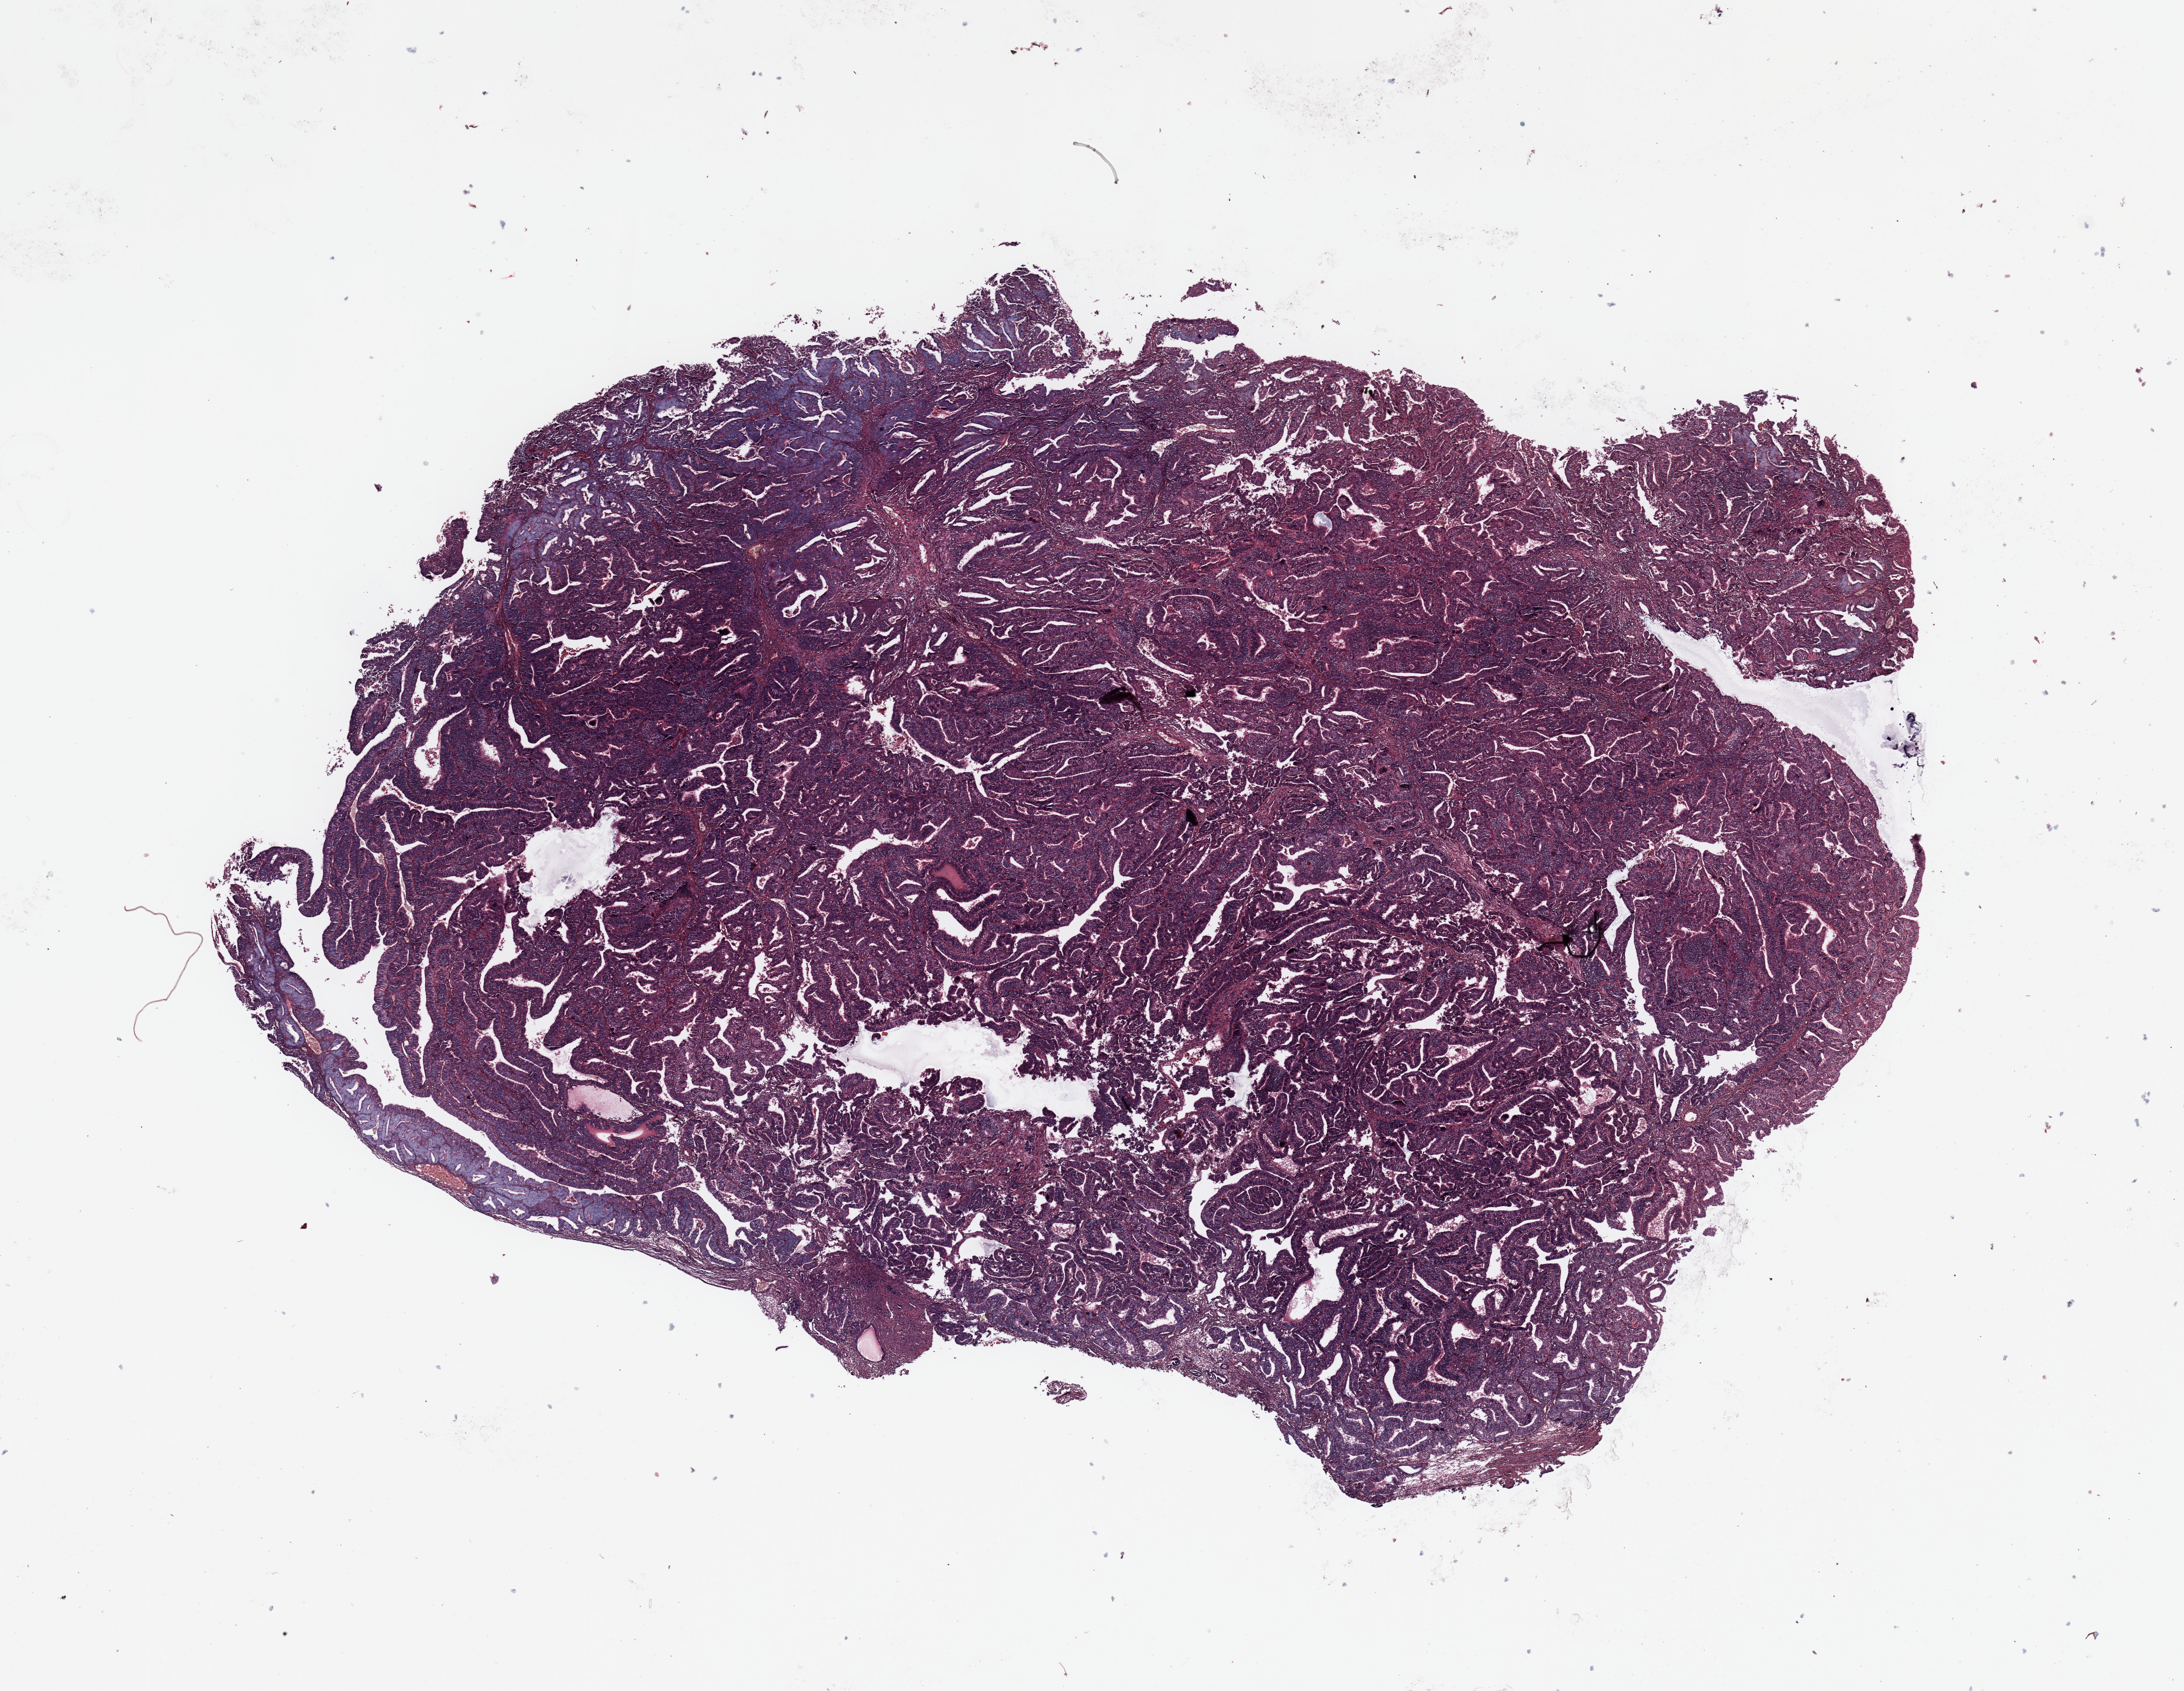
H&E whole-slide image, shown as a low-resolution overview of the whole scanned area (about 14.8 x 11.4 mm); tumour tissue sample, sampled site: uterus. 66-year-old female patient.
Diagnosis: Endometrioid adenocarcinoma, NOS.